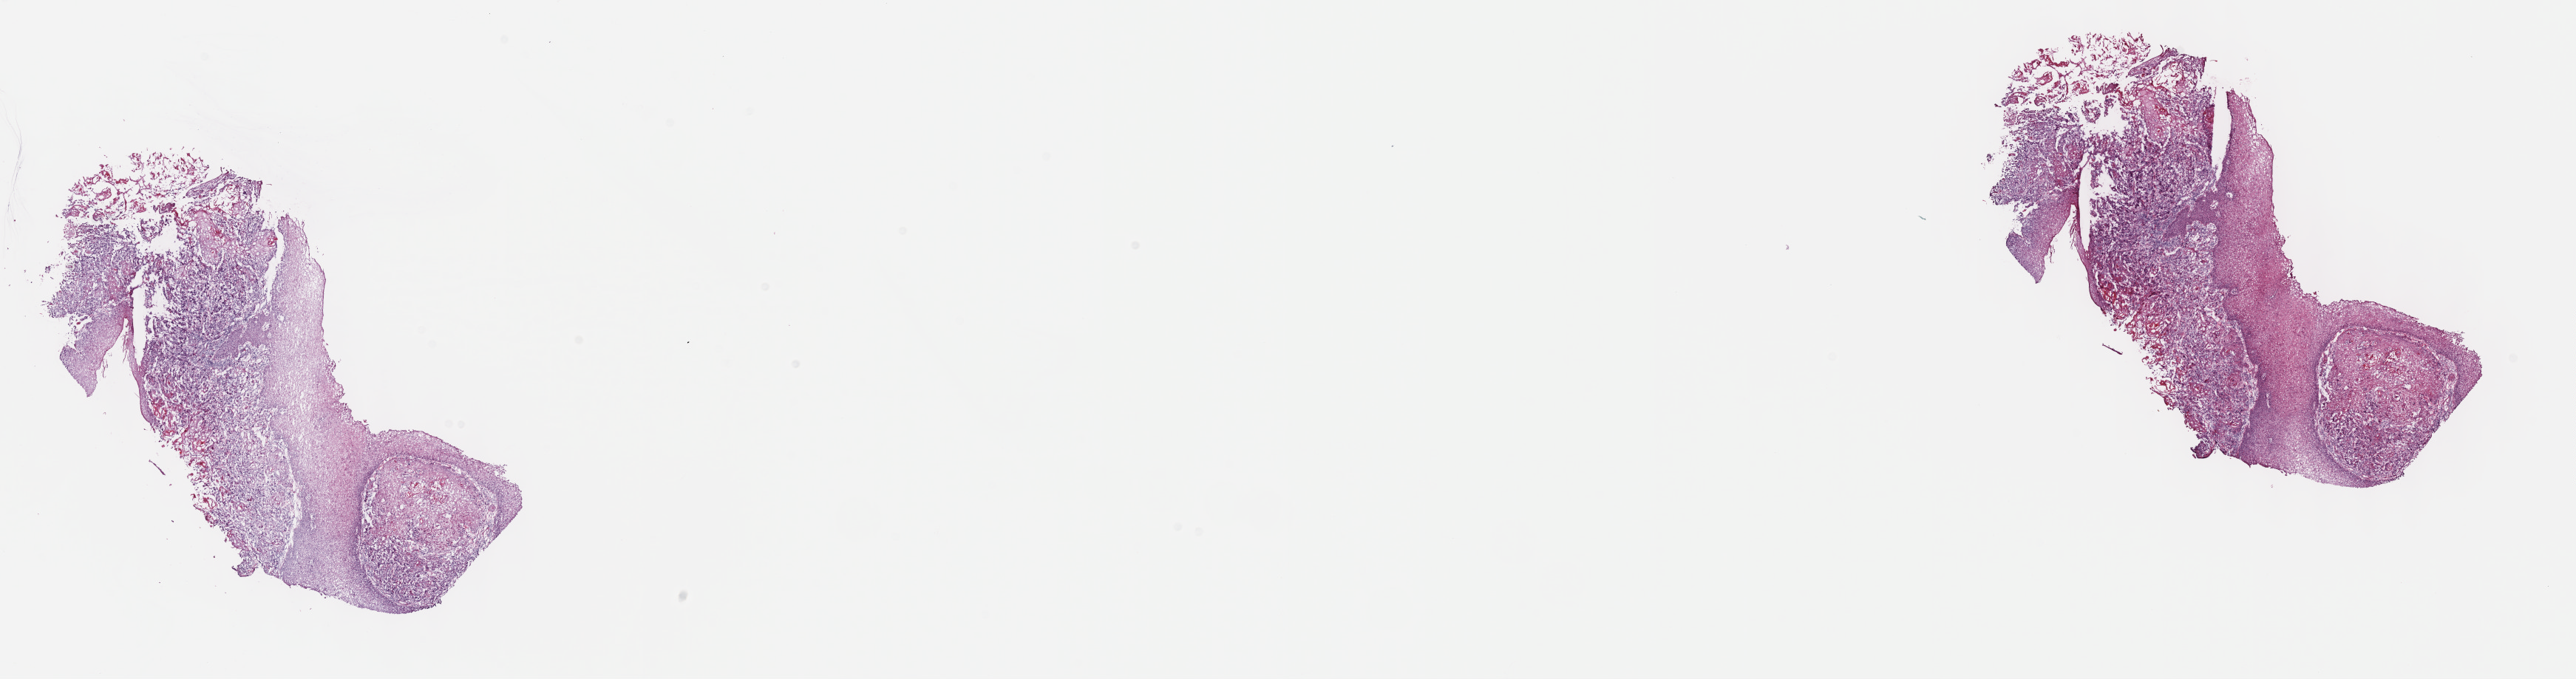
Whole-slide histology image, H&E, shown as a low-resolution overview of the whole scanned area (about 28.2 x 7.4 mm, acquisition: 40x scan); frozen section from the top of the tissue portion; primary tumour sample from the head and neck. Male, age 51 years at initial diagnosis. Histologic grade: G2 (moderately differentiated). Slide review estimates, as recorded: tumour cells 65%, tumour nuclei 65%, normal cells 35%, stromal cells 0%, necrosis 0%. Infiltration values recorded for this section: lymphocyte infiltration 3%, monocyte infiltration 0%, neutrophil infiltration 0%.
• diagnosis: Squamous cell carcinoma, keratinizing, NOS (larynx, NOS)
• AJCC pathologic stage: IVA (7th edition)
• laterality: midline